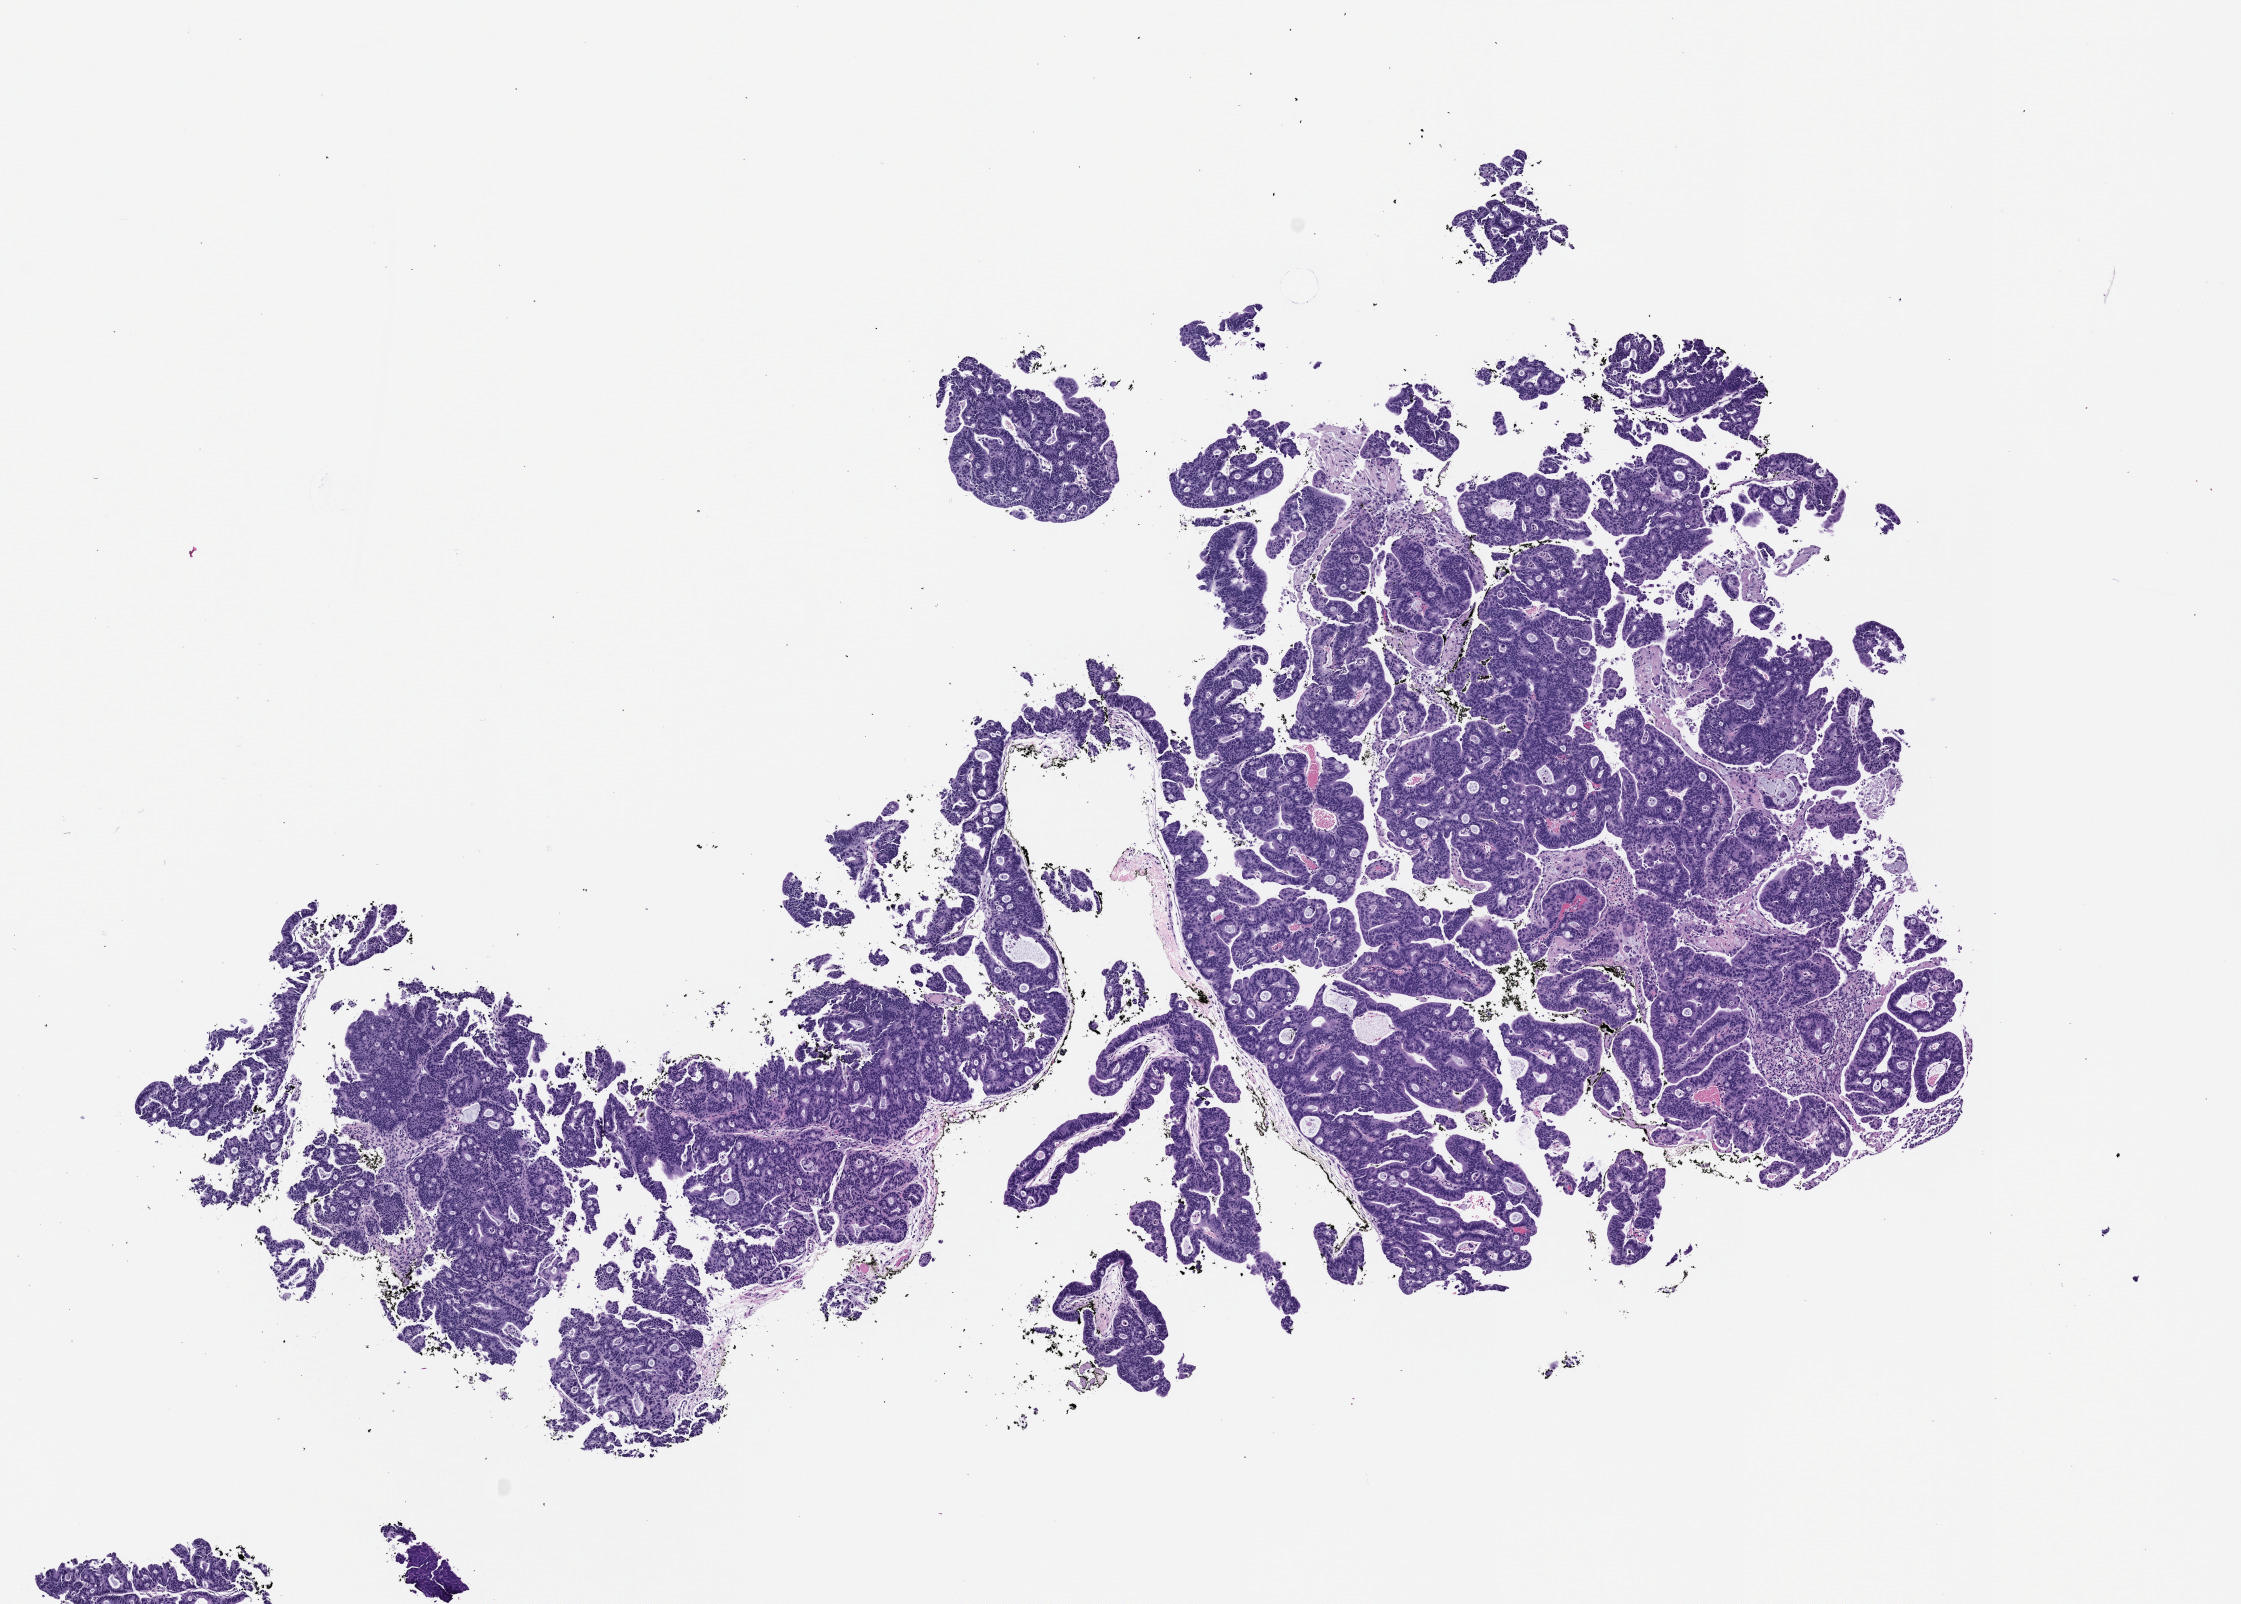
Haematoxylin and eosin whole-slide image of a patient-derived xenograft (PDX) tumor grown in a mouse, passage 2 — low-resolution overview of the scanned area, about 9.0 x 6.5 mm. Formalin-fixed, paraffin-embedded (FFPE) tissue. Tumor site category: rectum.
Originating patient diagnosis: Rectal Adenocarcinoma.